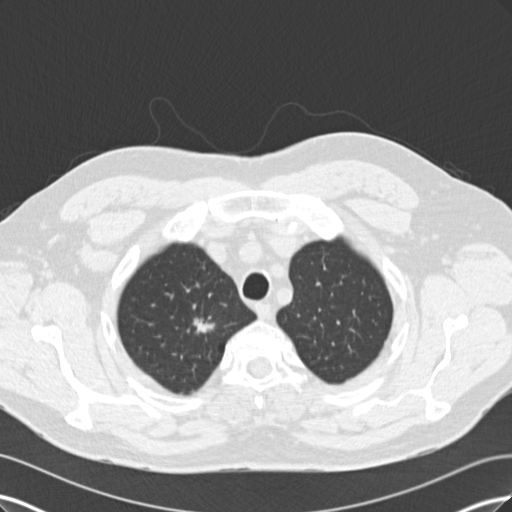
Low-dose screening chest CT, one axial slice; position 148 of 171 along the scan axis; lung window (W 1500 / L -600 HU); 2 mm slice thickness; 512 × 512 image matrix, field of view 360 × 360 mm.
Structures marked on this image (manually delineated by an expert):
- lesion 1 (tumor, upper lobe of right lung): bounding box [x1, y1, x2, y2] px = [187, 317, 215, 333]